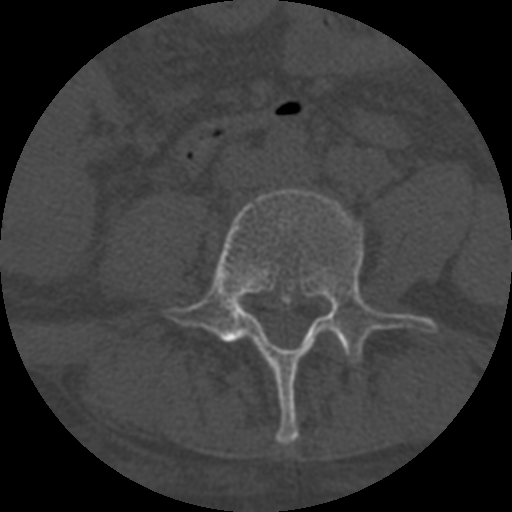
CT including the spine, one axial slice. Slice 210 of 708 in the series (ordered by position). One of 3 acquisitions stored at this slice position. Bone window (W 1800 / L 400 HU). 1.25 mm slice thickness. 512 × 512 image matrix, field of view 160 × 160 mm. Patient age 55 years. Case-level facts recorded for this patient, not image findings: primary cancer: colon; vertebrae with lytic lesions (as recorded): T12, L1, L5.
Structures marked on this image (semi-automatically segmented with operator editing):
- L4 vertebra: bounding box (x1, y1, x2, y2) in pixels: (165, 188, 437, 445)